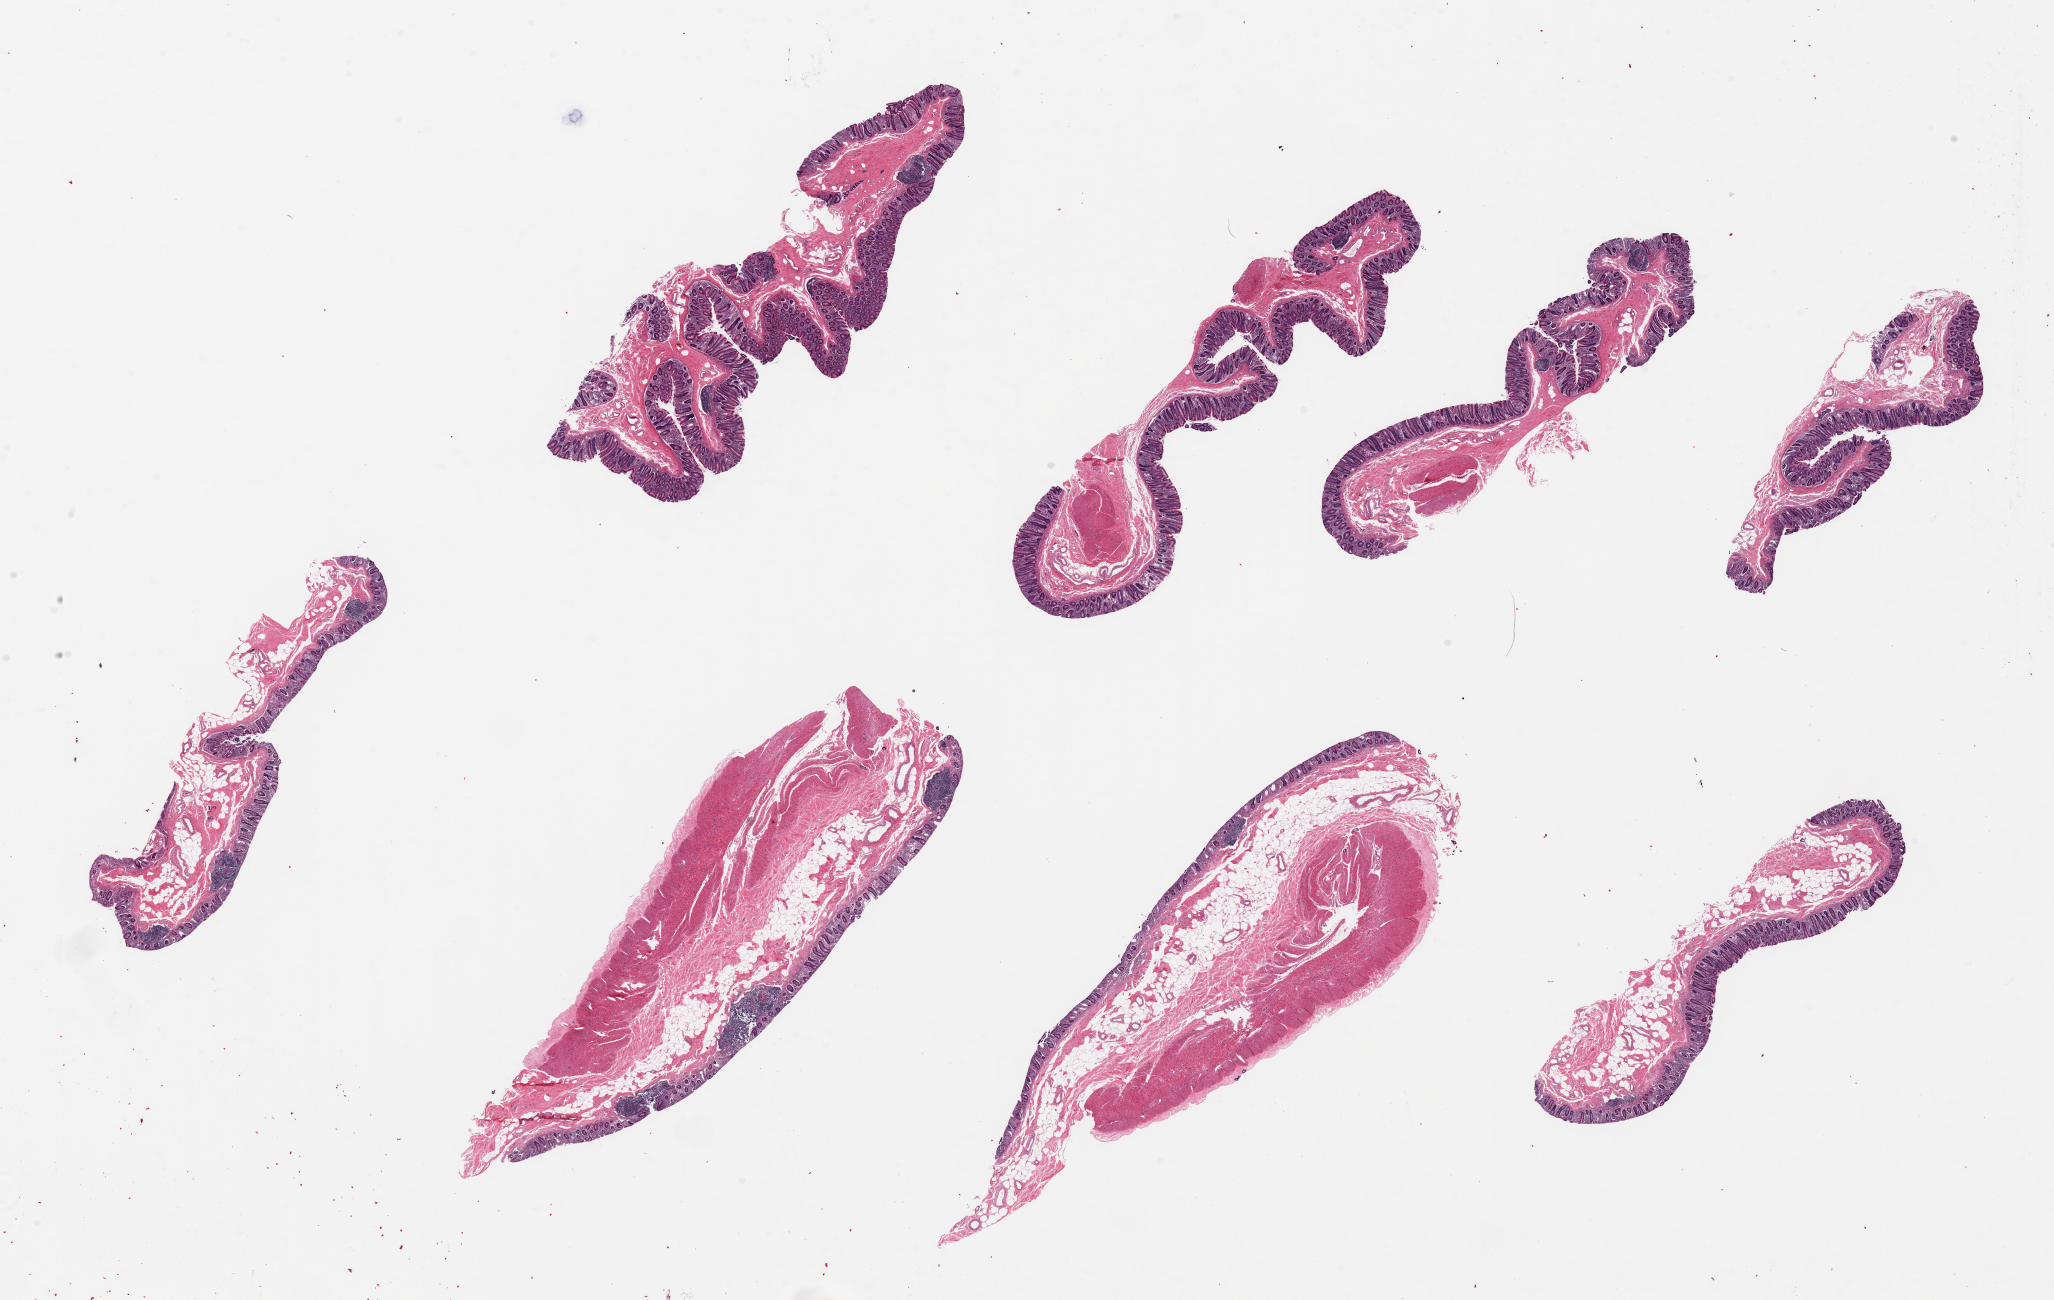
Whole-slide image, H&E stain, brightfield — shown as a low-resolution overview of the whole scanned area (about 32.5 x 20.6 mm, slide scanned at 20x); PAXgene-fixed, paraffin-embedded tissue; section of ileum (target tissue); donor tissue sample. Donor sex: male.
Reviewer comment on this tissue sample: 8 pieces ~8x2mm. Muscle present, Mainly mucosa, rare lymphoid nodules evident.